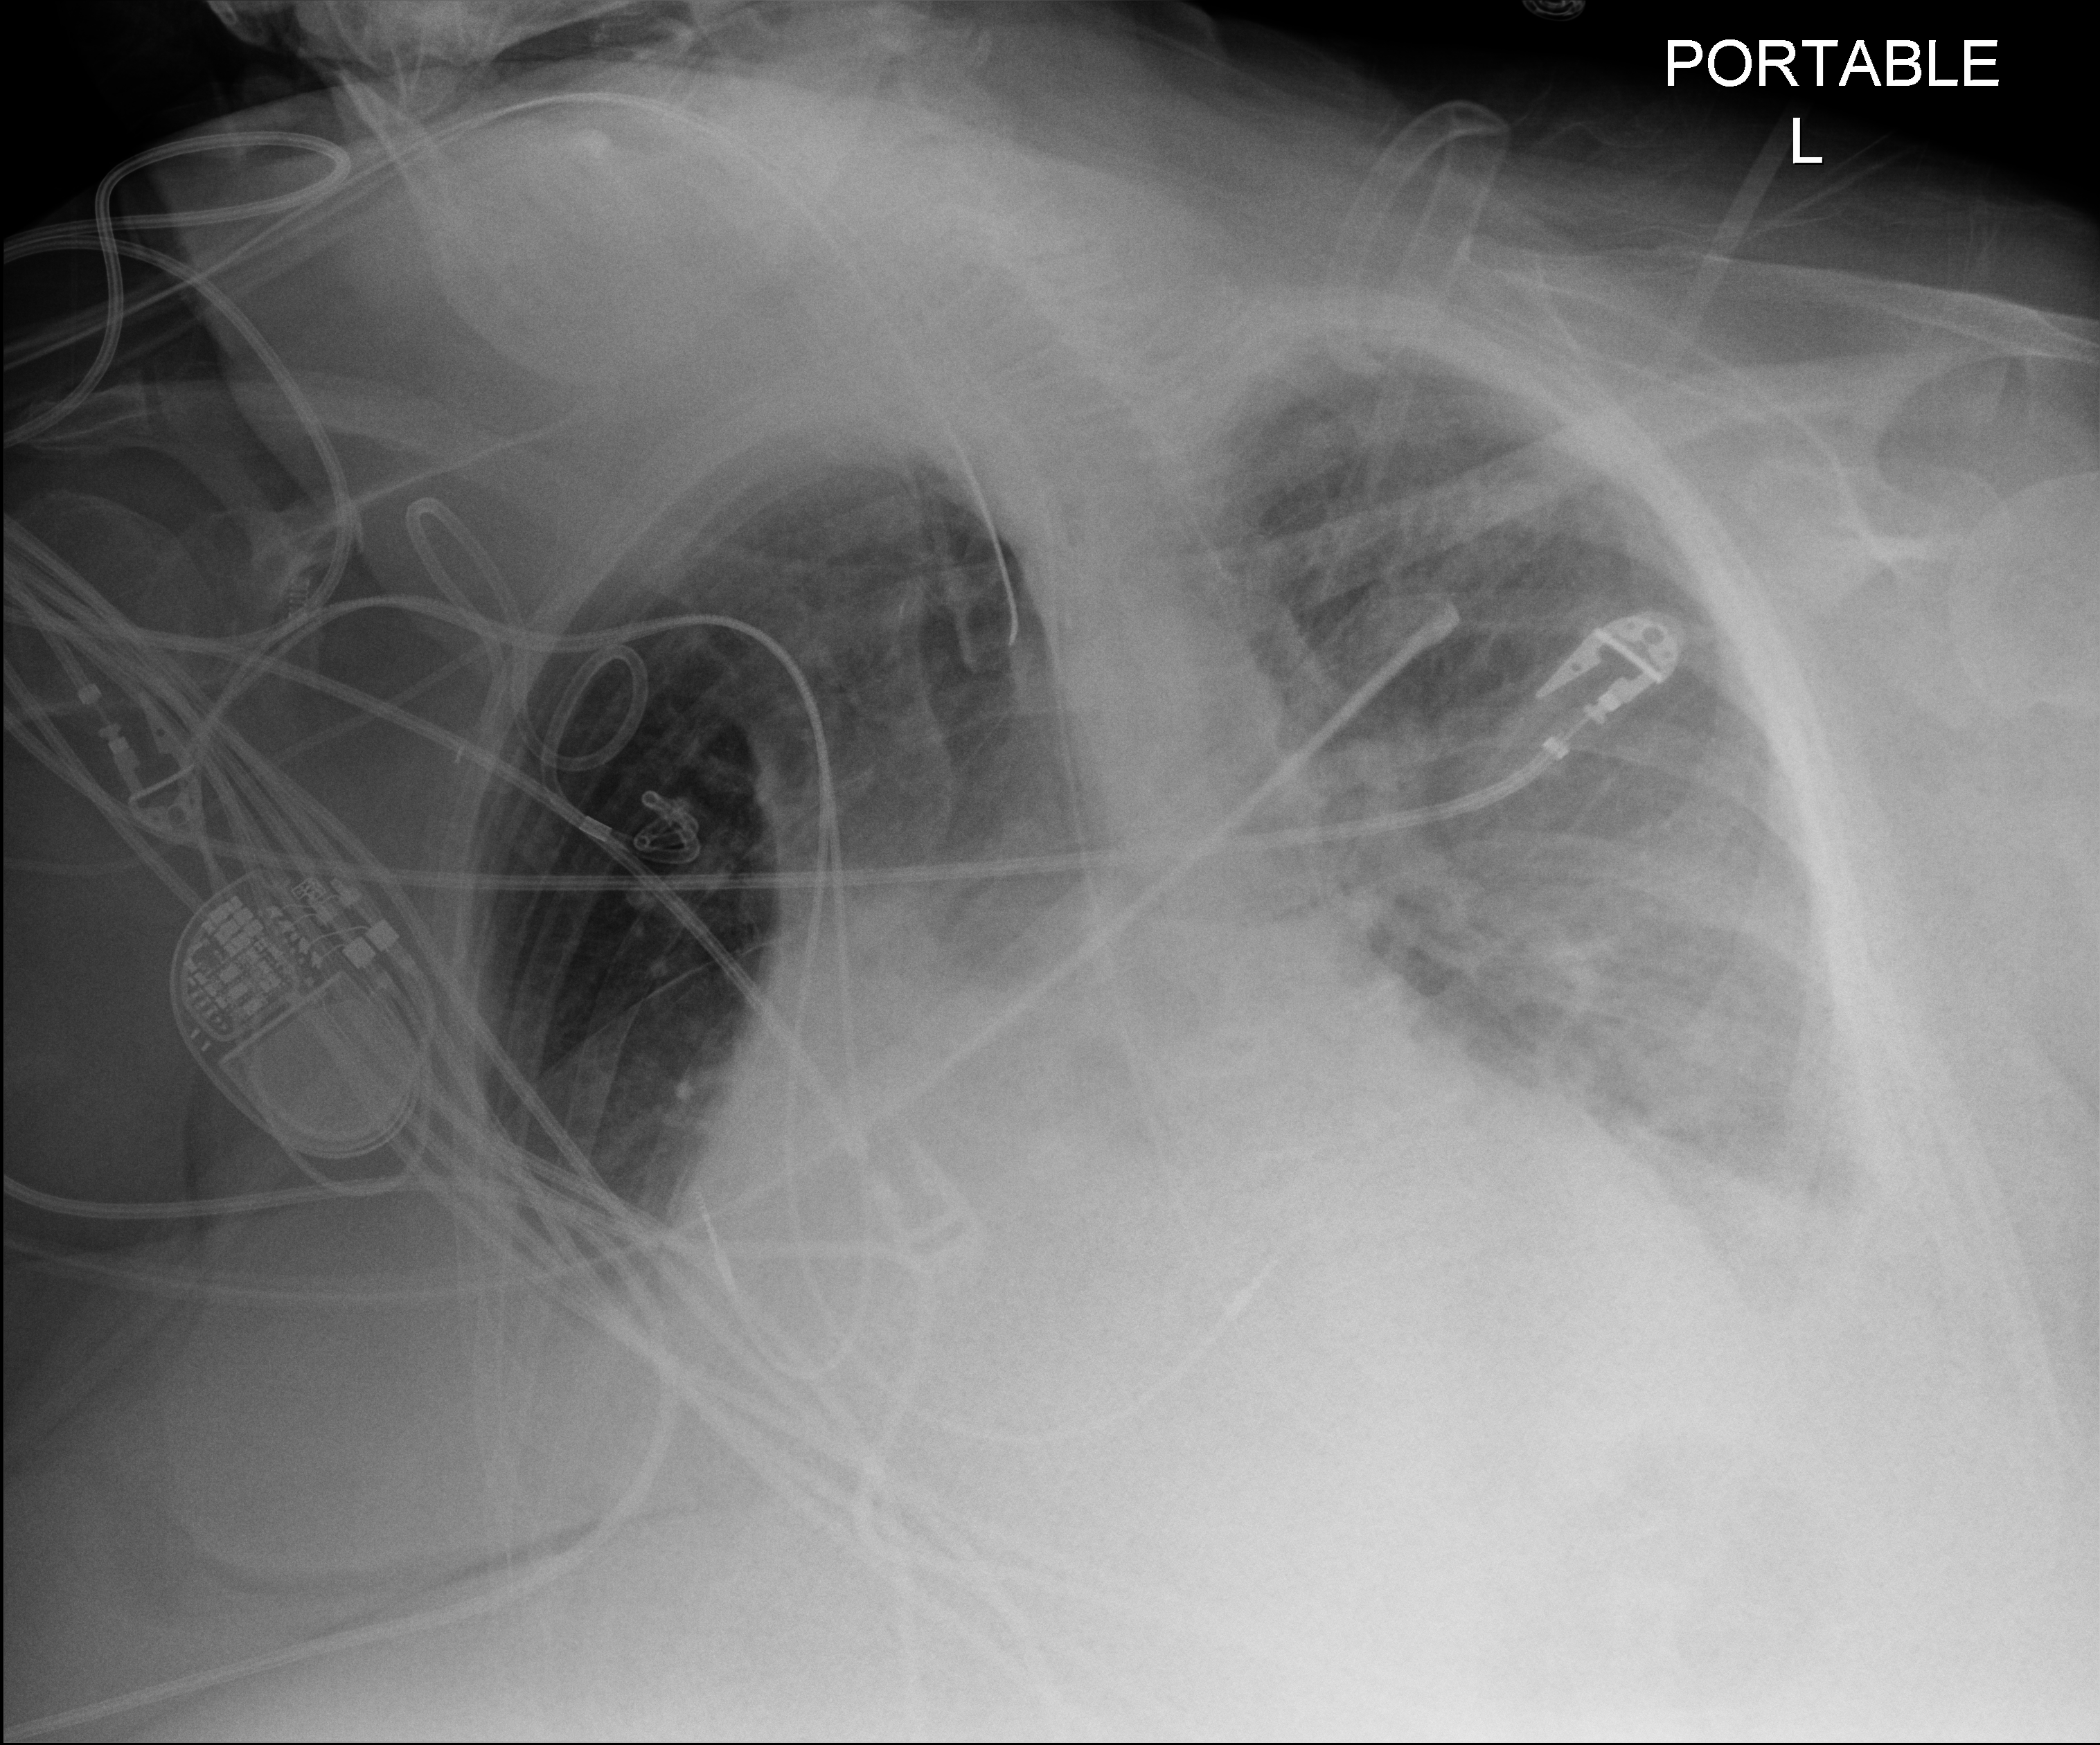
Bedside chest radiograph (digital radiography), anteroposterior (AP) projection. Patient hospitalised with COVID-19; female, aged 75–90 years.
From the hospital-stay record, not from the radiograph (when in the stay this image was taken is not recorded): diabetes (admission record): yes; mechanically ventilated during this hospital stay: yes.